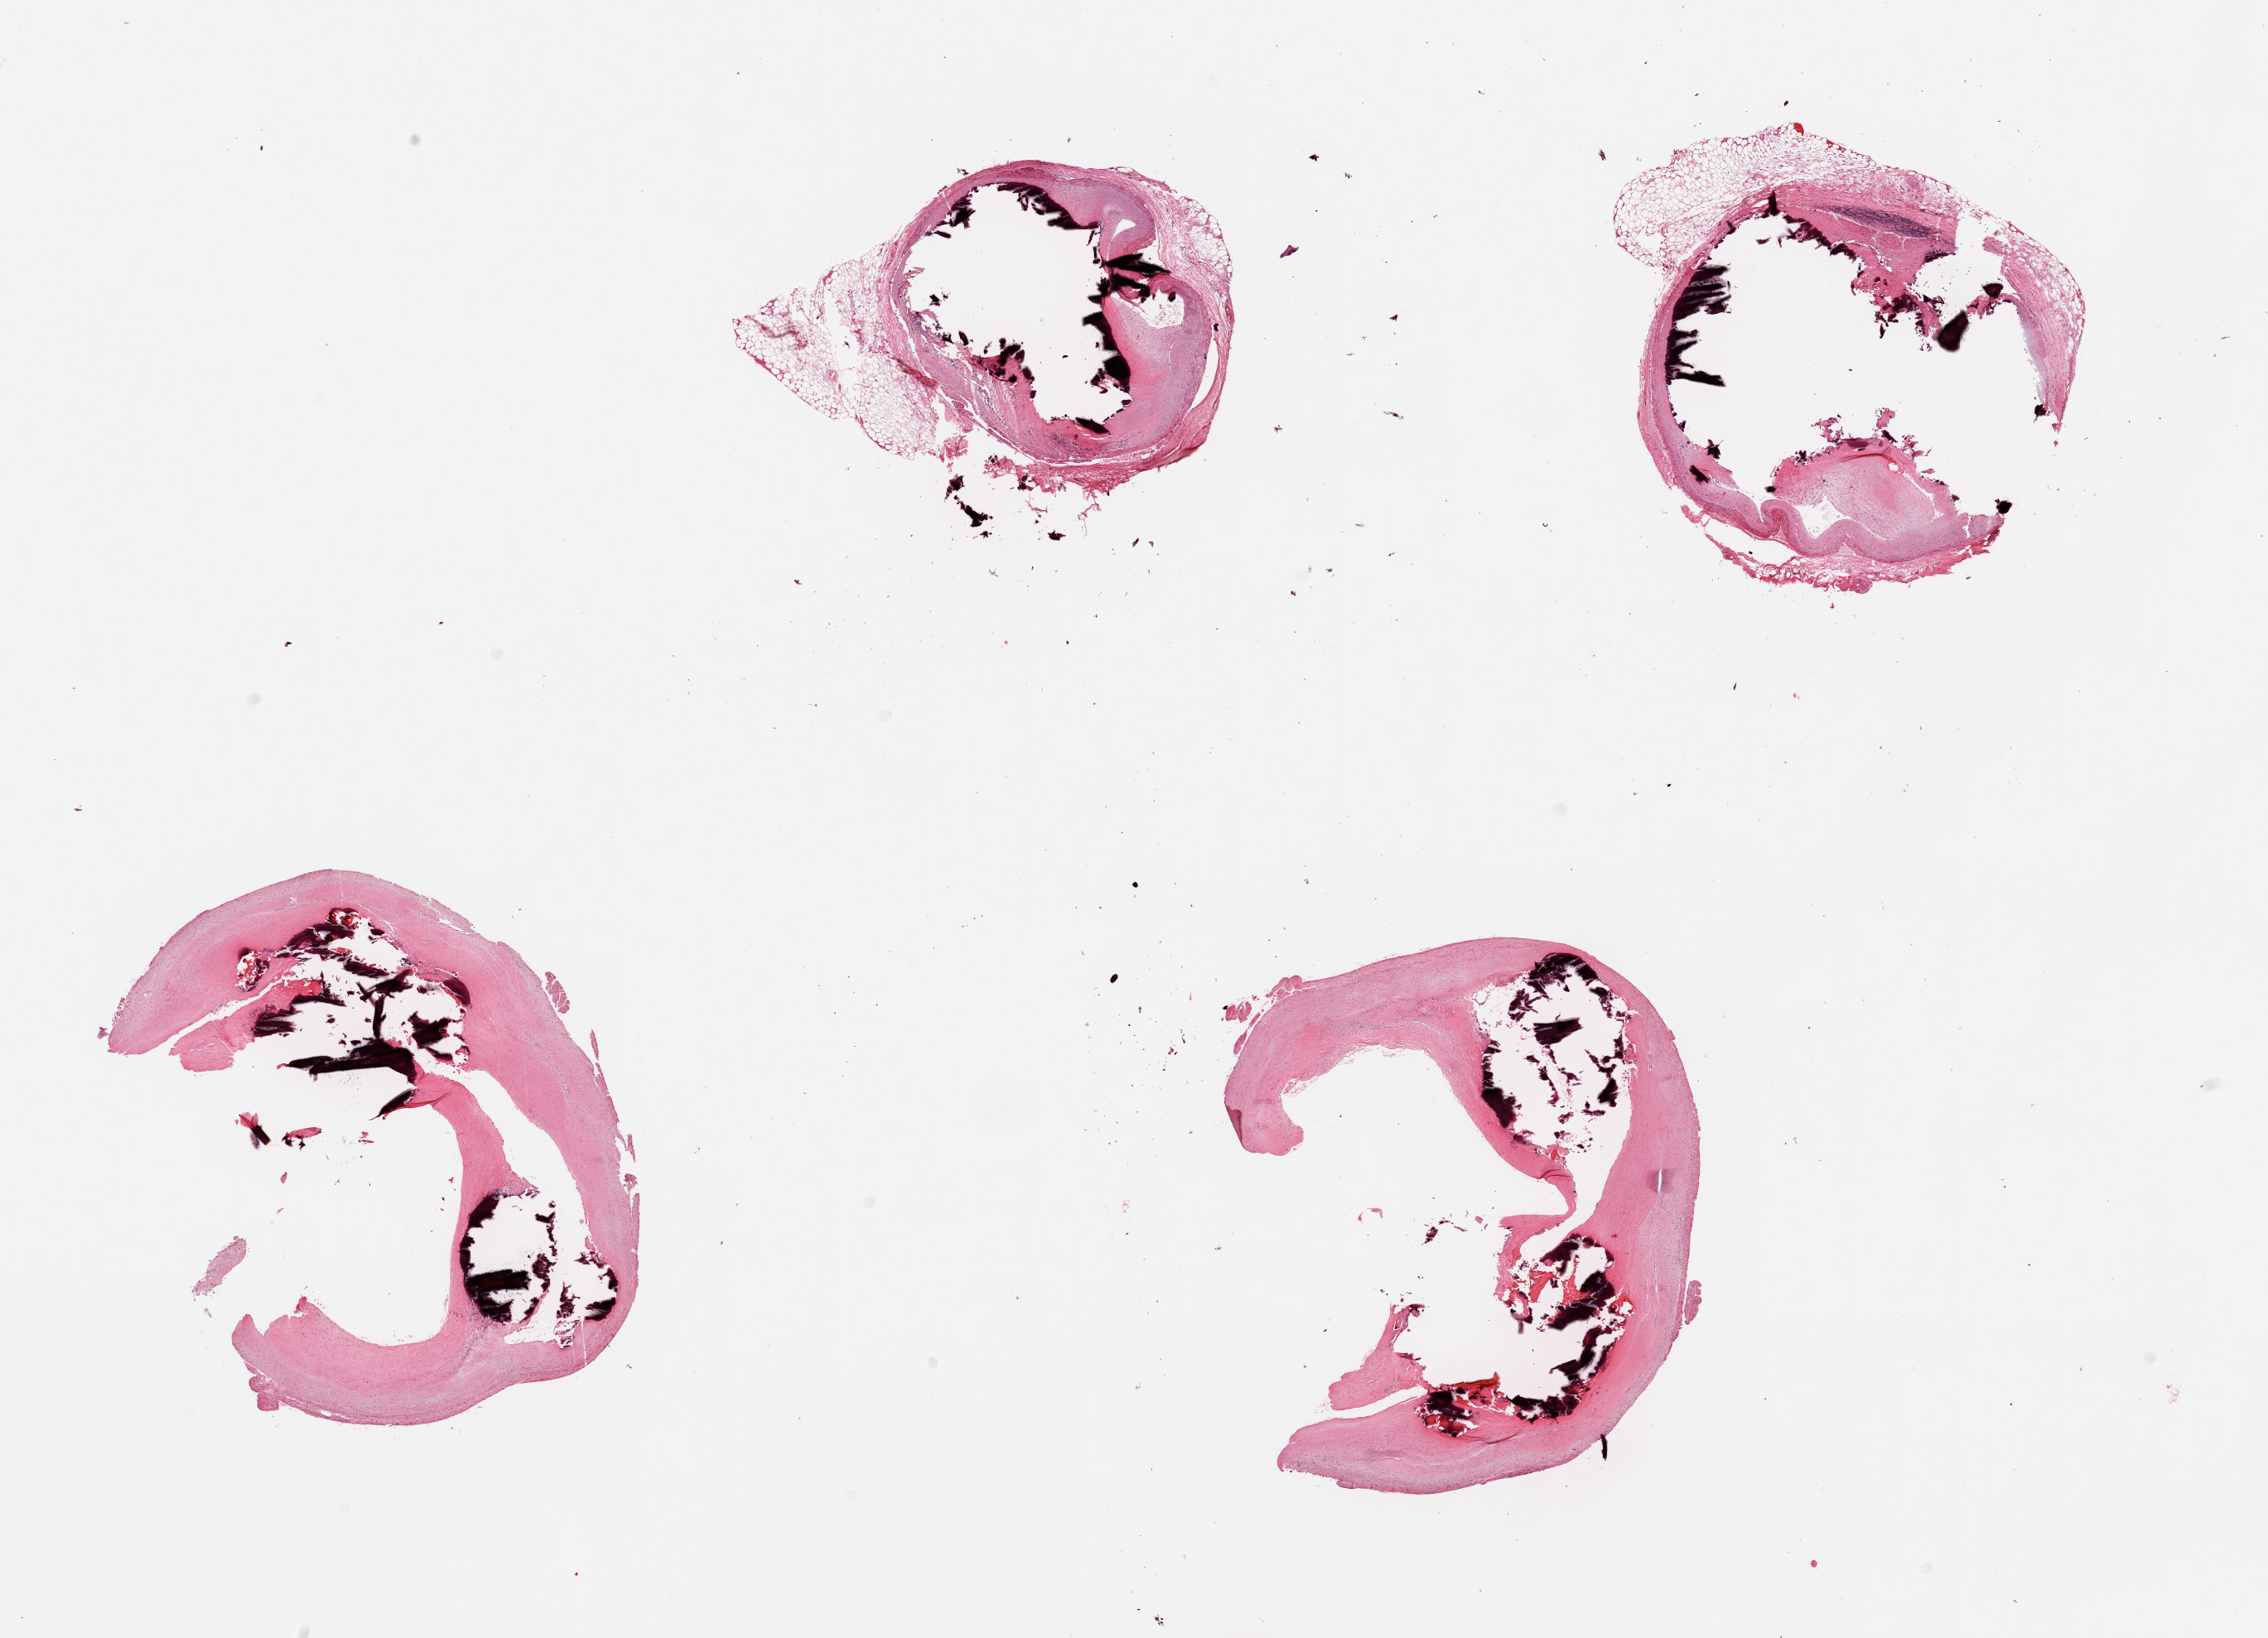
Digitized haematoxylin and eosin-stained section — a low-resolution overview of the entire scanned area, about 21.7 x 15.6 mm. PAXgene-fixed, paraffin-embedded tissue. Section of coronary artery (target tissue). Donor tissue sample. Donor sex: male.
* review note (as recorded): 4 pieces; calcific atherosclerosis (fragmented) with luminal narrowing, attached fat up to 1.4mm